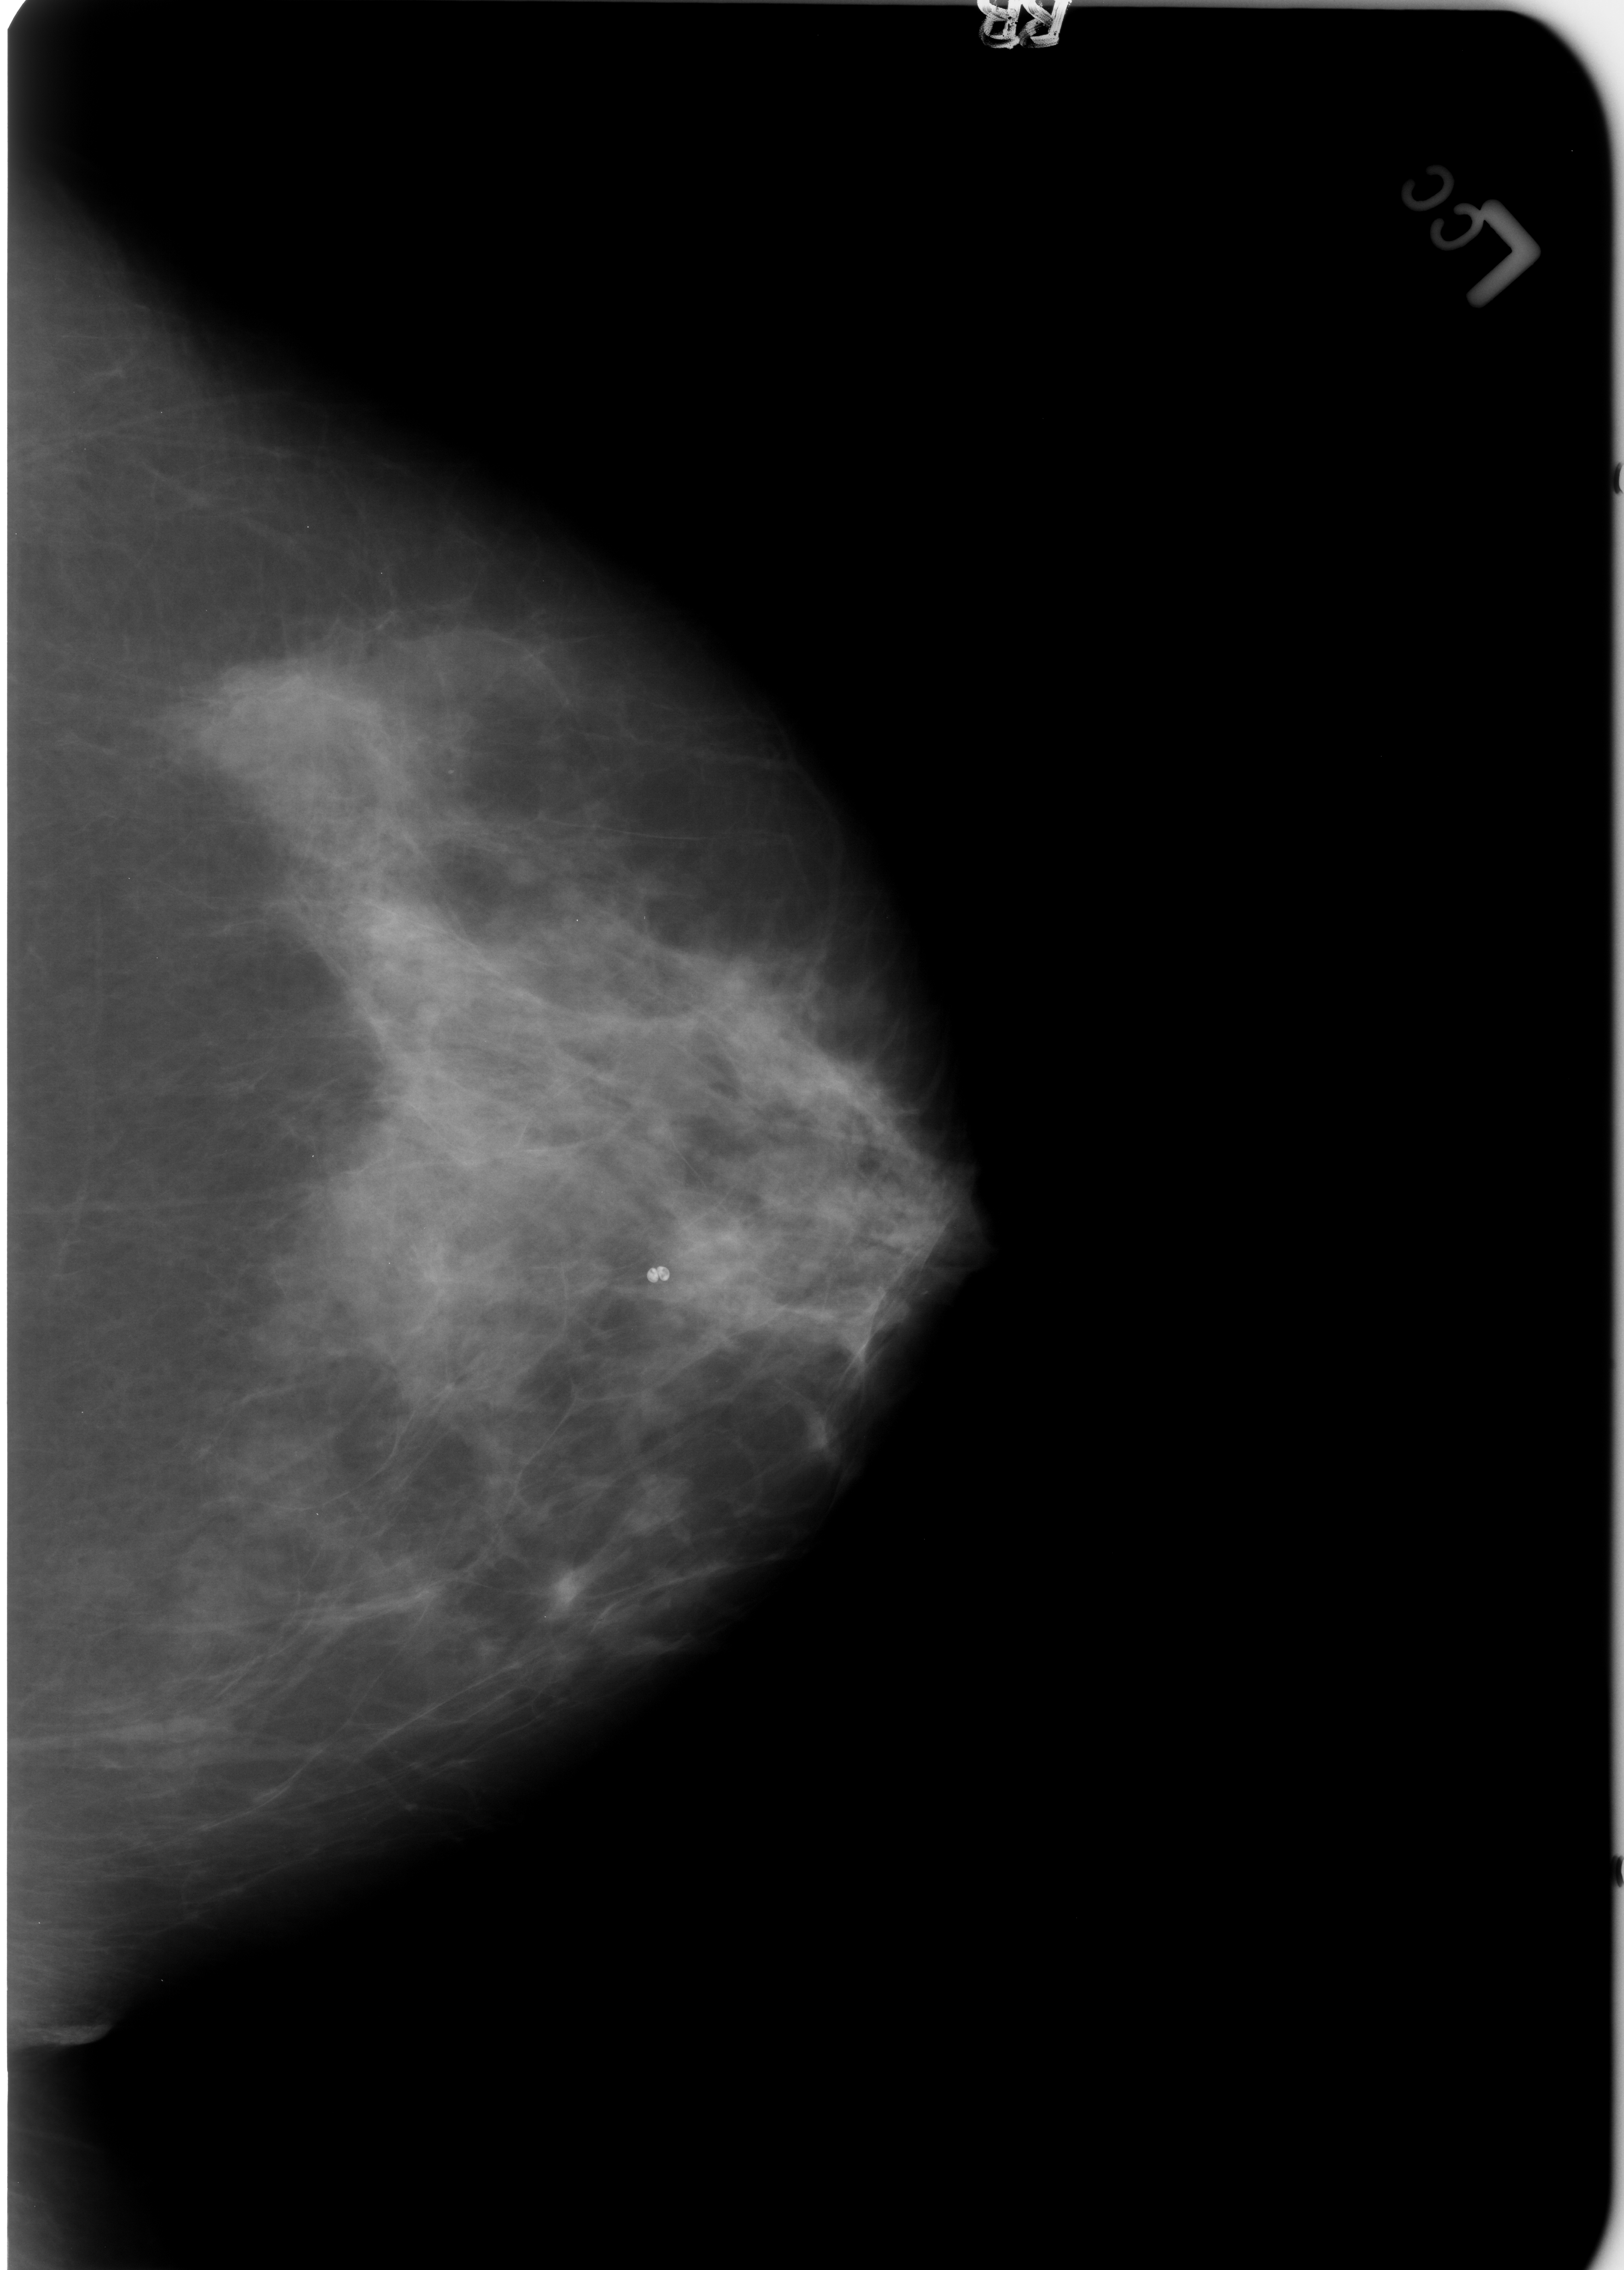
Digitized screen-film mammogram. Left breast. Craniocaudal (CC) view. Breast composition: heterogeneously dense (BI-RADS density category 3 of 4). 1624 × 2270 image matrix.
Expert-marked regions of interest on this film, with their recorded descriptors:
- calcifications, morphology lucent center; BI-RADS assessment category 2; outcome (as recorded, no biopsy): benign without callback (not worked up further): box from (x=639, y=1259) to (x=682, y=1309) px